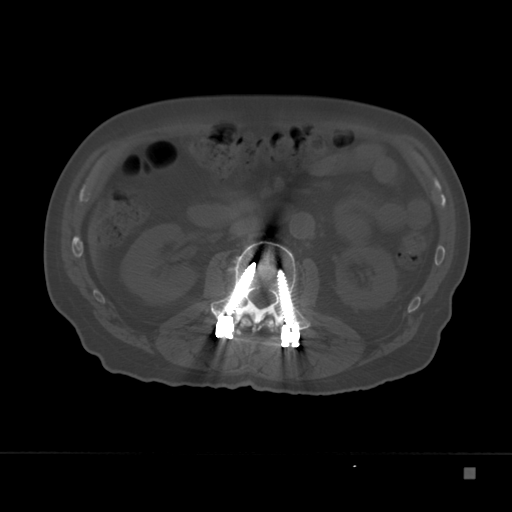
CT including the spine, one axial slice. Position 92 of 332 along the scan axis. Reconstruction kernel Br40s. Bone window (W 1800 / L 400 HU). 512 × 512 image matrix, field of view 389 × 389 mm. Male patient, age 72 years. From the clinical record (not read from this slice): primary cancer: skeletal.
Annotated regions visible in this slice (semi-automatic segmentation, software-assisted and operator-edited):
- L1 vertebra: bounding box <239,315,275,330> (left, top, right, bottom; pixels)
- L2 vertebra: <210,242,316,331>